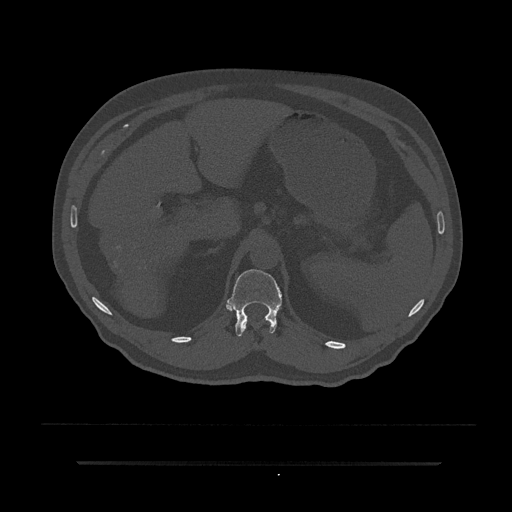
CT including the spine, one axial slice. Position 226 of 797 along the scan axis. Reconstruction kernel Br40s/3. 120 kVp. Bone window (W 1800 / L 400 HU). 0.5 mm slice thickness. 512 × 512 image matrix, field of view 464 × 464 mm. Patient: male, 59 years. Case-level facts recorded for this patient, not image findings: primary cancer: bile ducts; vertebrae with lytic lesions (as recorded): T10.
Structures marked on this image (semi-automatically segmented with operator editing):
- T12 vertebra: bounding box <227,269,282,337> (left, top, right, bottom; pixels)